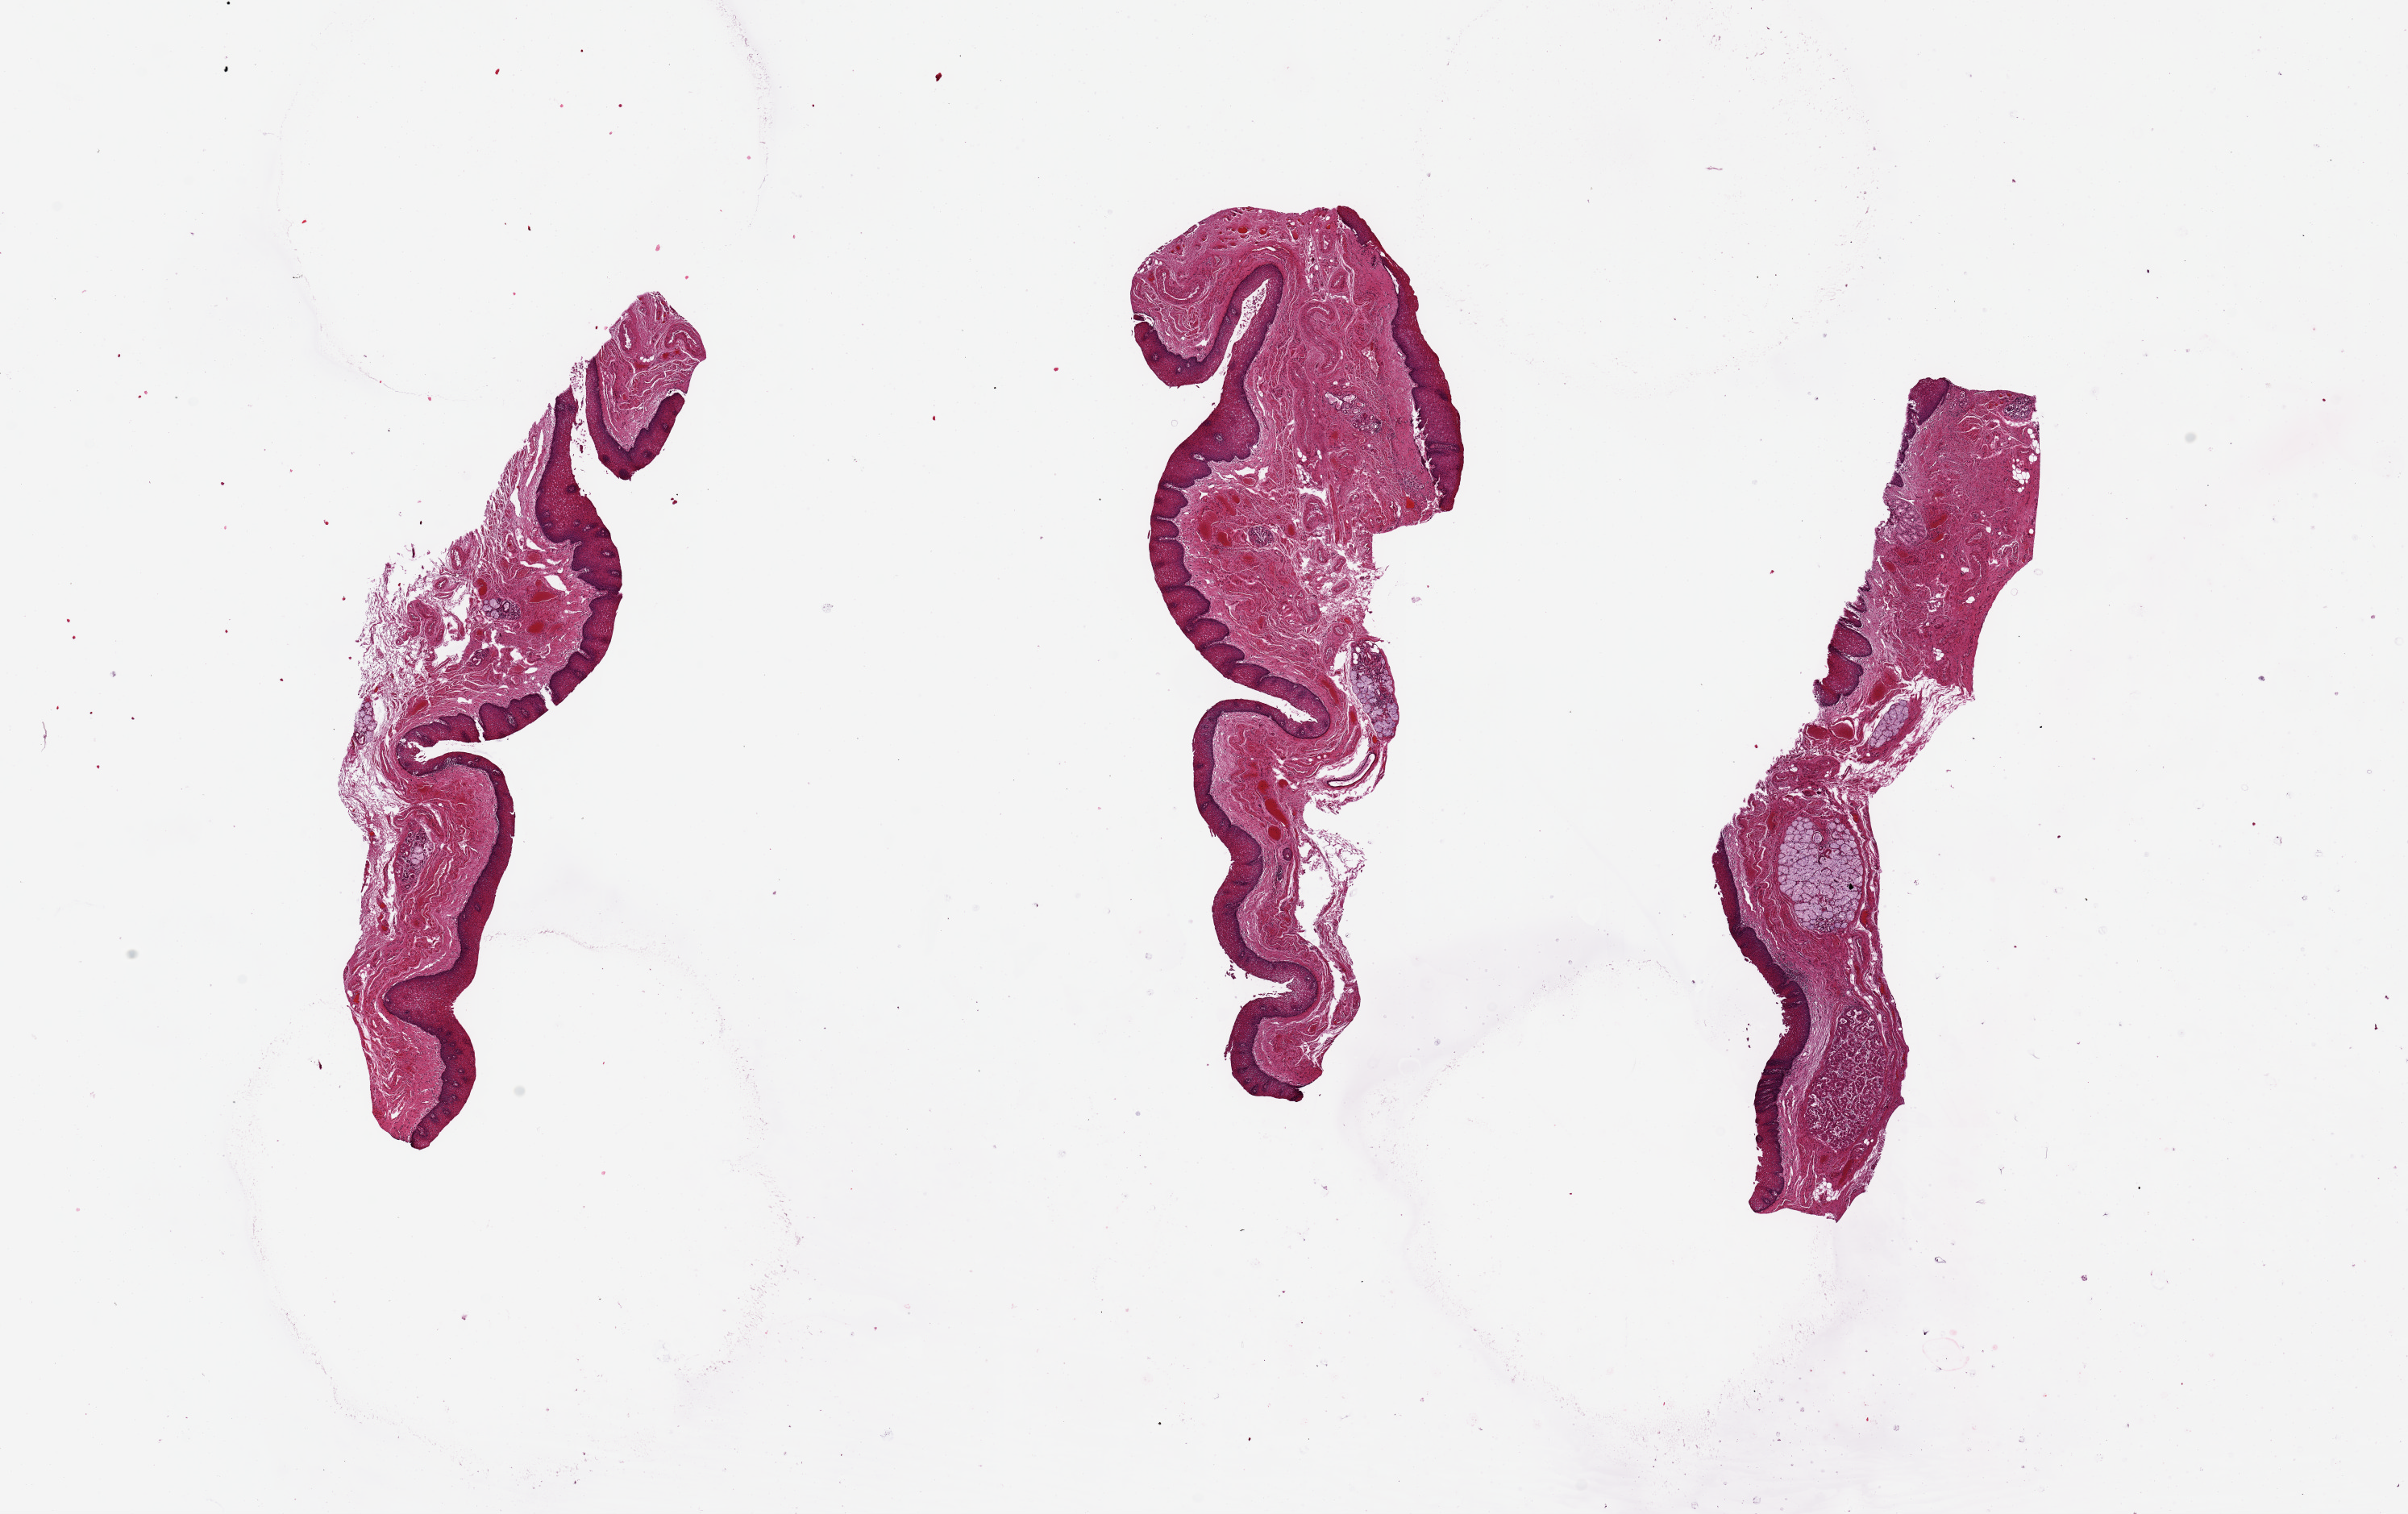
Whole-slide image, H&E stain, whole scanned area (about 23.6 x 14.9 mm) shown as a low-resolution overview. PAXgene-fixed paraffin-embedded (PFPE) section. Target tissue: esophageal mucous membrane. Donor tissue sample.
Review note (as recorded): MUSCULARIS, NOT MUCOSA; 3 pieces 12x4.5 mm.